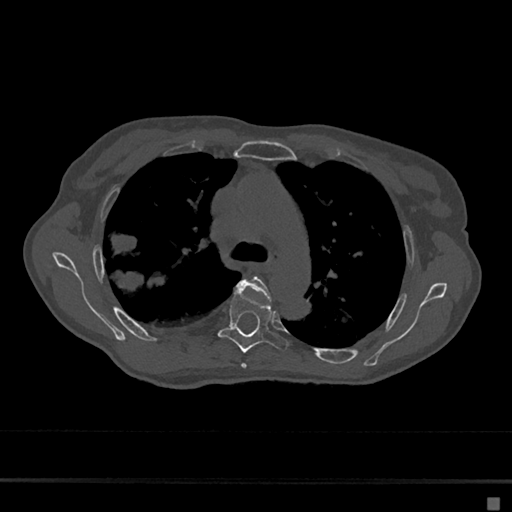
CT including the spine, one axial slice; position 468 of 797 along the scan axis; reconstruction kernel Br40s/3; bone window (W 1800 / L 400 HU); 0.5 mm slice thickness; 512 × 512 image matrix, field of view 360 × 360 mm. Patient: female, 68 years. Case-level facts recorded for this patient, not image findings: primary cancer: renal.
Annotated regions visible in this slice (semi-automatically segmented with operator editing):
- T4 vertebra: bounding box (x1, y1, x2, y2) in pixels: (237, 276, 272, 369)
- T5 vertebra: (218, 290, 288, 353)